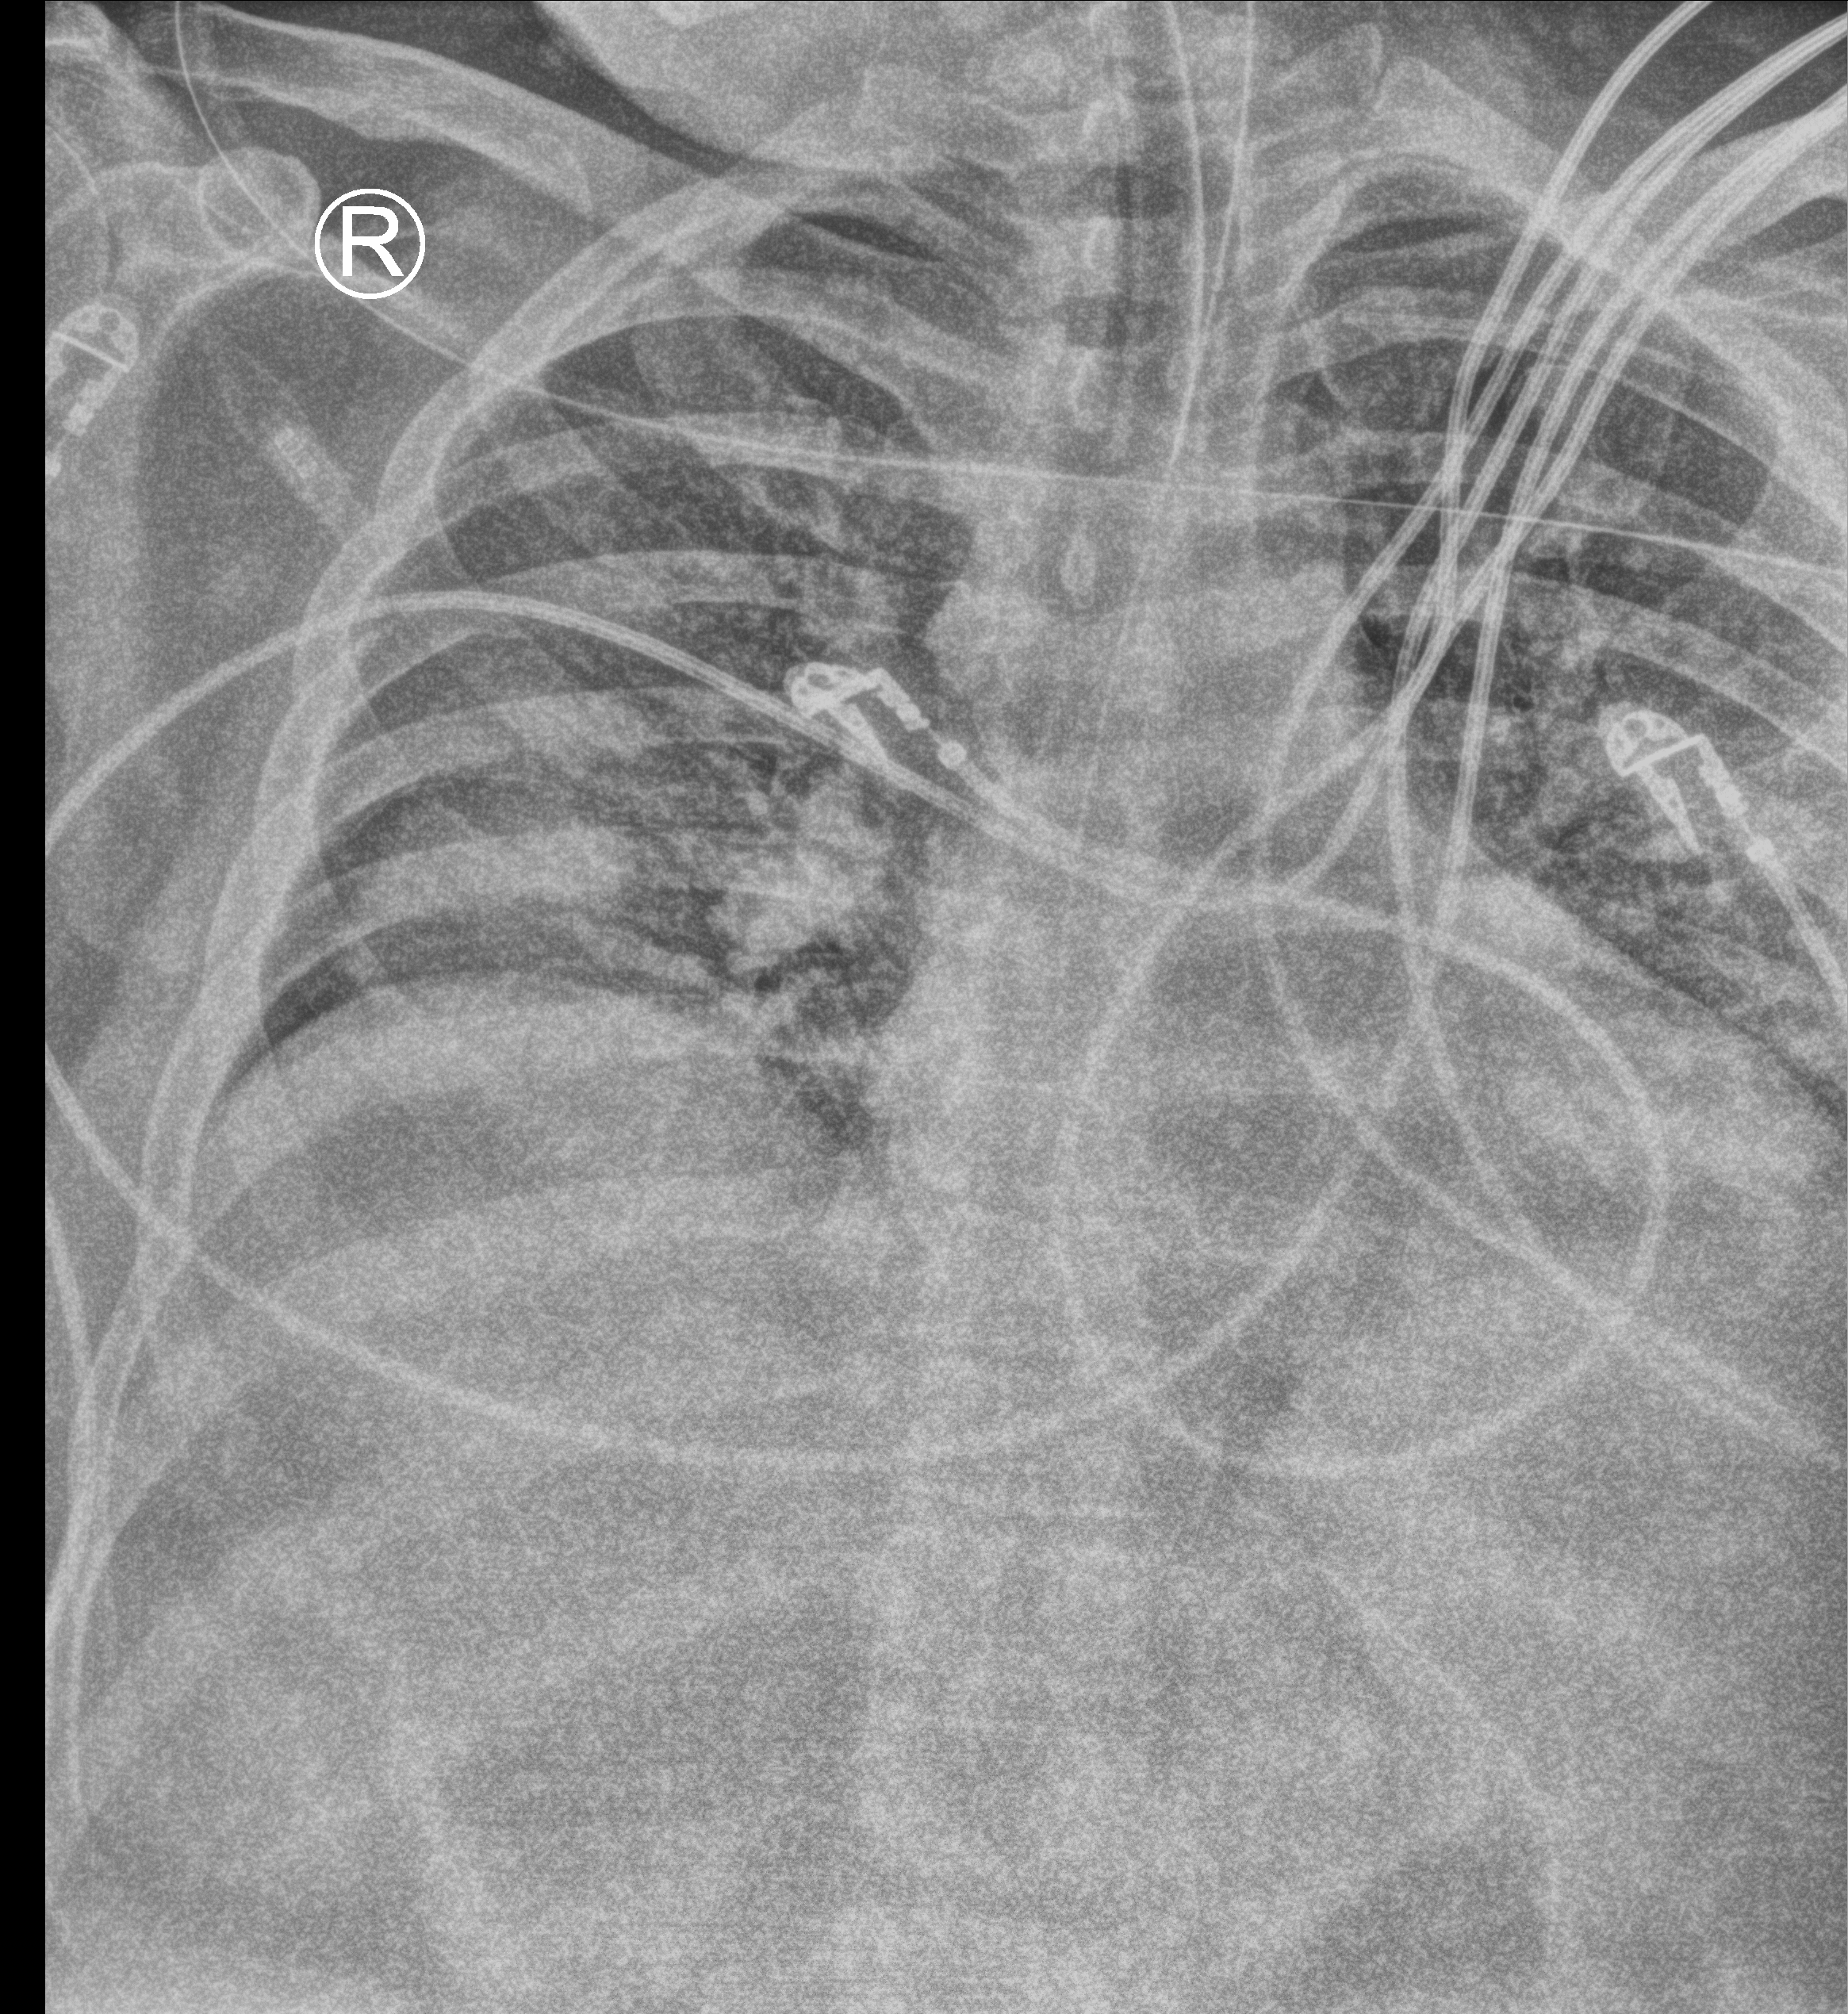
Portable chest radiograph; anteroposterior (AP) projection. Patient hospitalised with COVID-19; male, aged 18–59 years.
Admission-level facts for this patient (not findings on this image; timing relative to this image not recorded): diabetes (admission record): no.